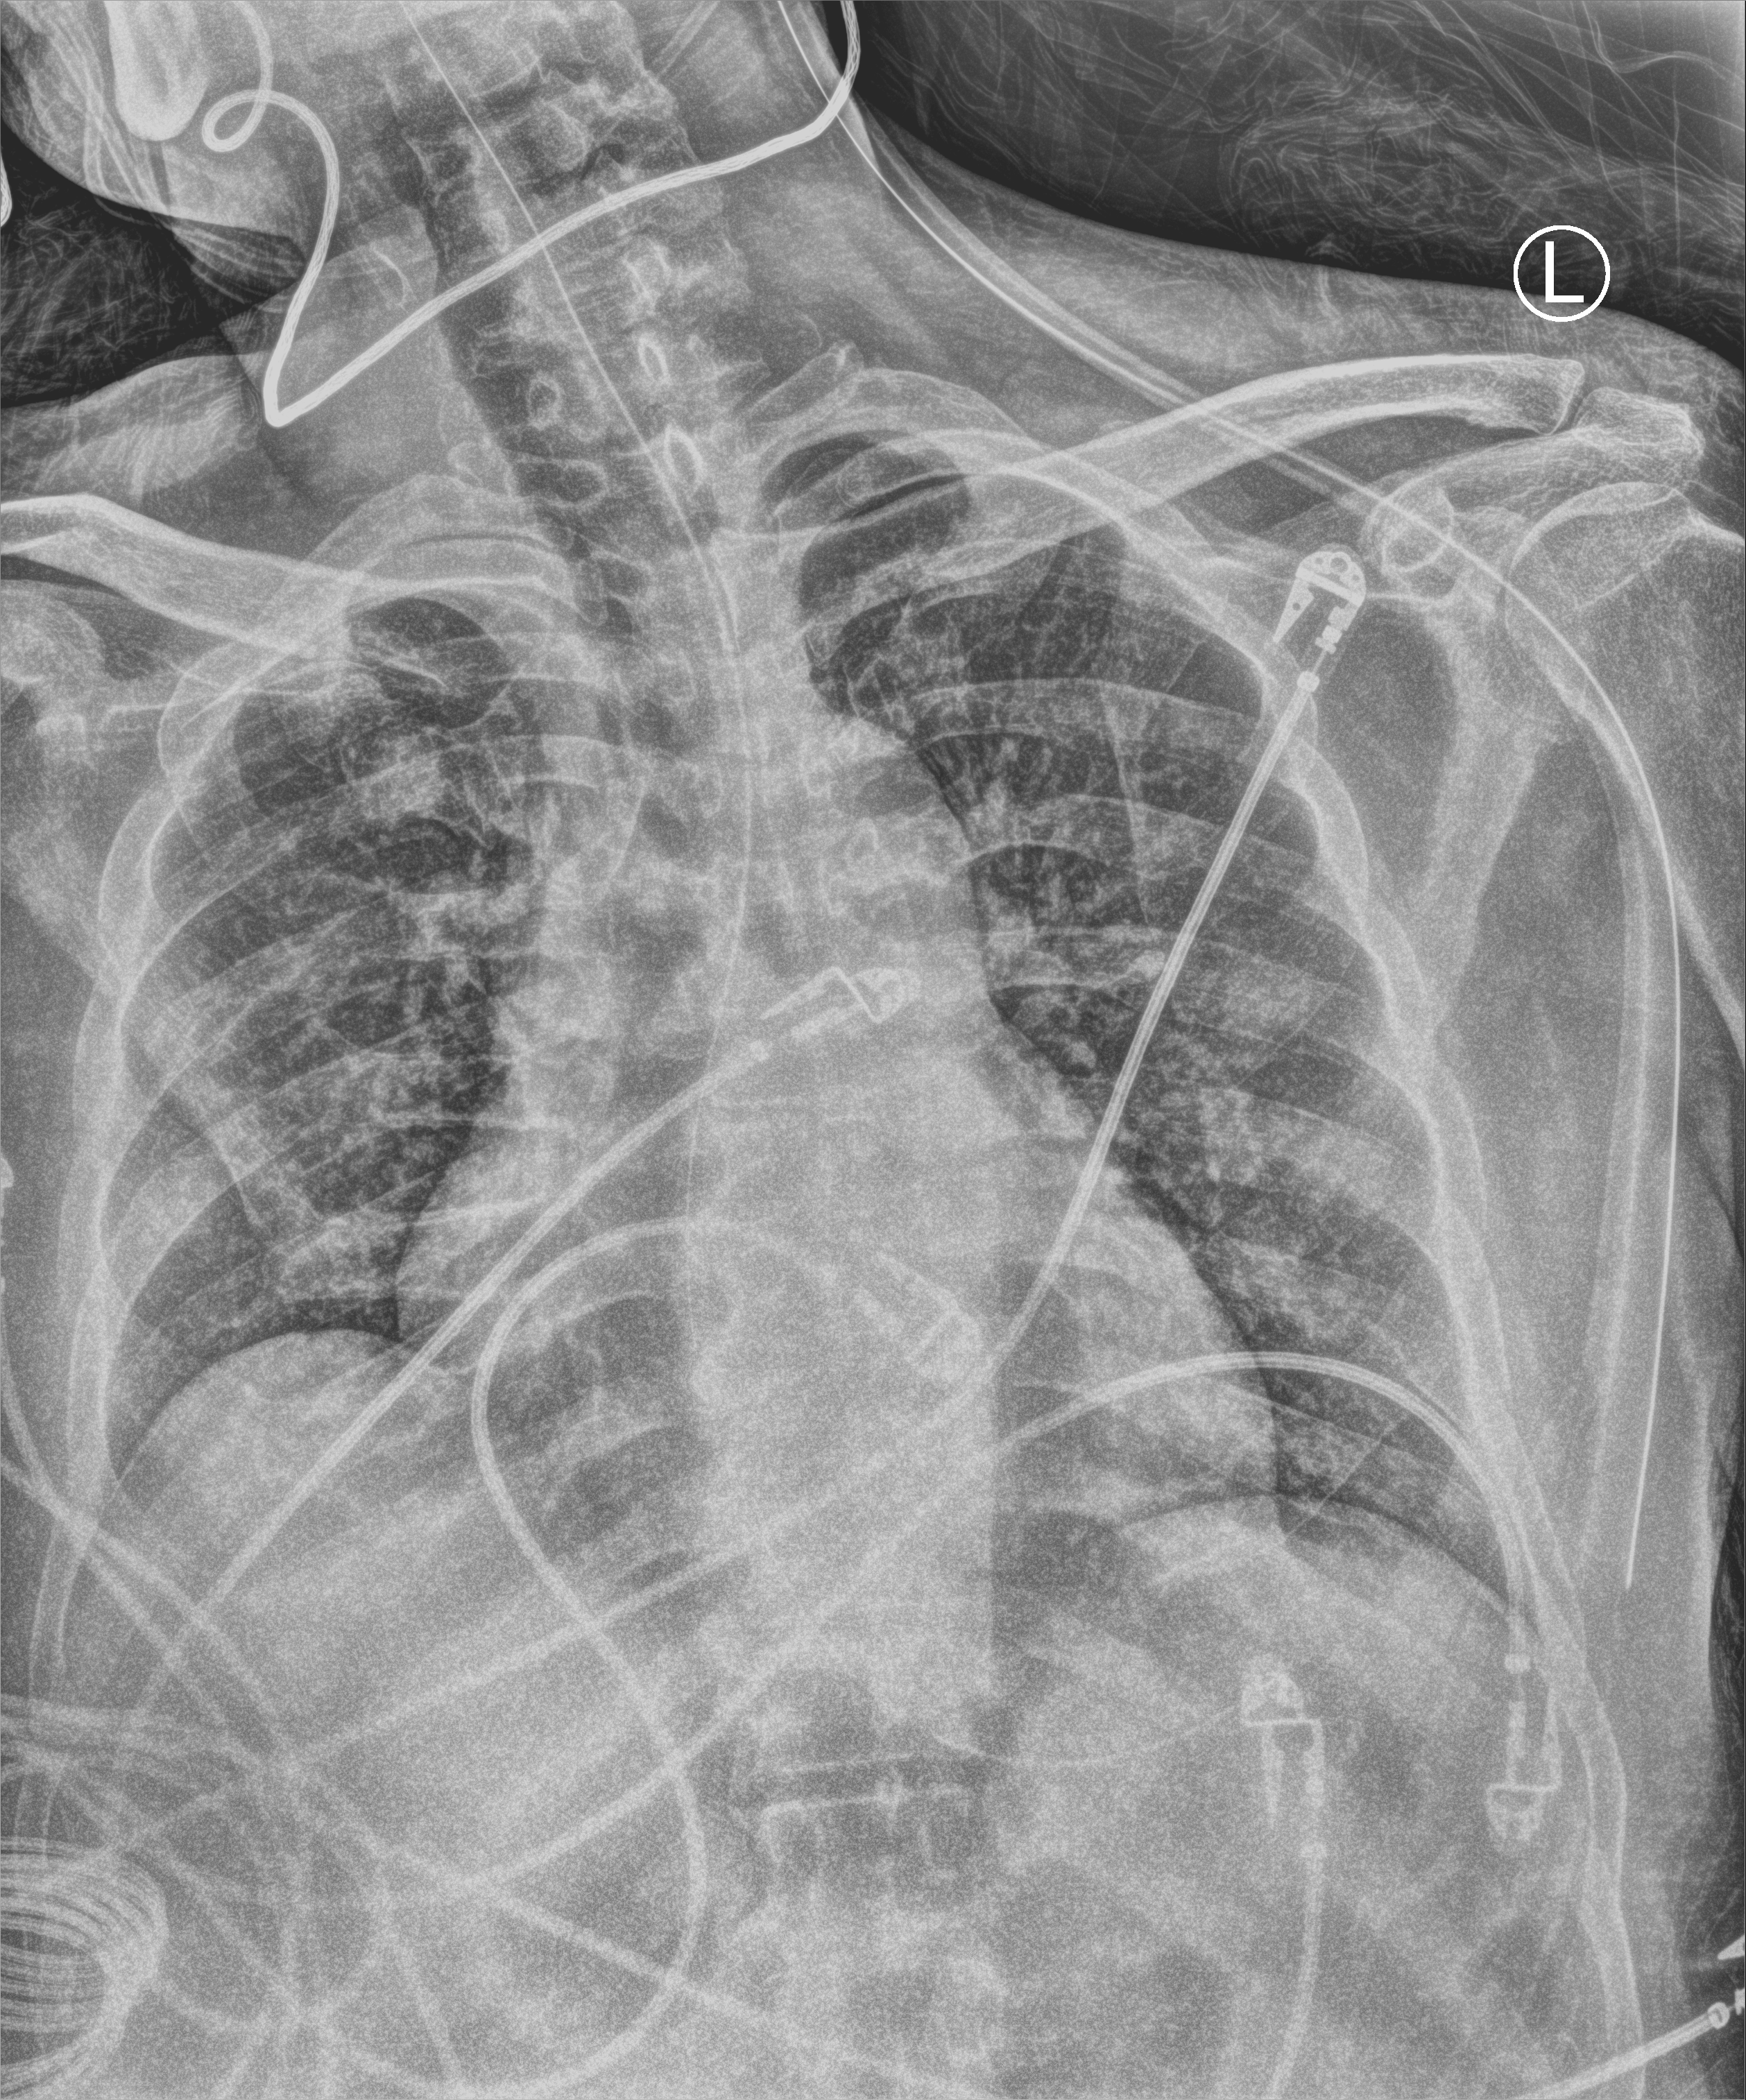
Bedside chest radiograph (computed radiography), anteroposterior (AP) projection. Patient hospitalised with COVID-19, aged 18–59 years.
From the hospital-stay record, not from the radiograph (when in the stay this image was taken is not recorded):
- COPD (admission record): no
- mechanically ventilated during this hospital stay: yes
- admitted to intensive care during this hospital stay: yes